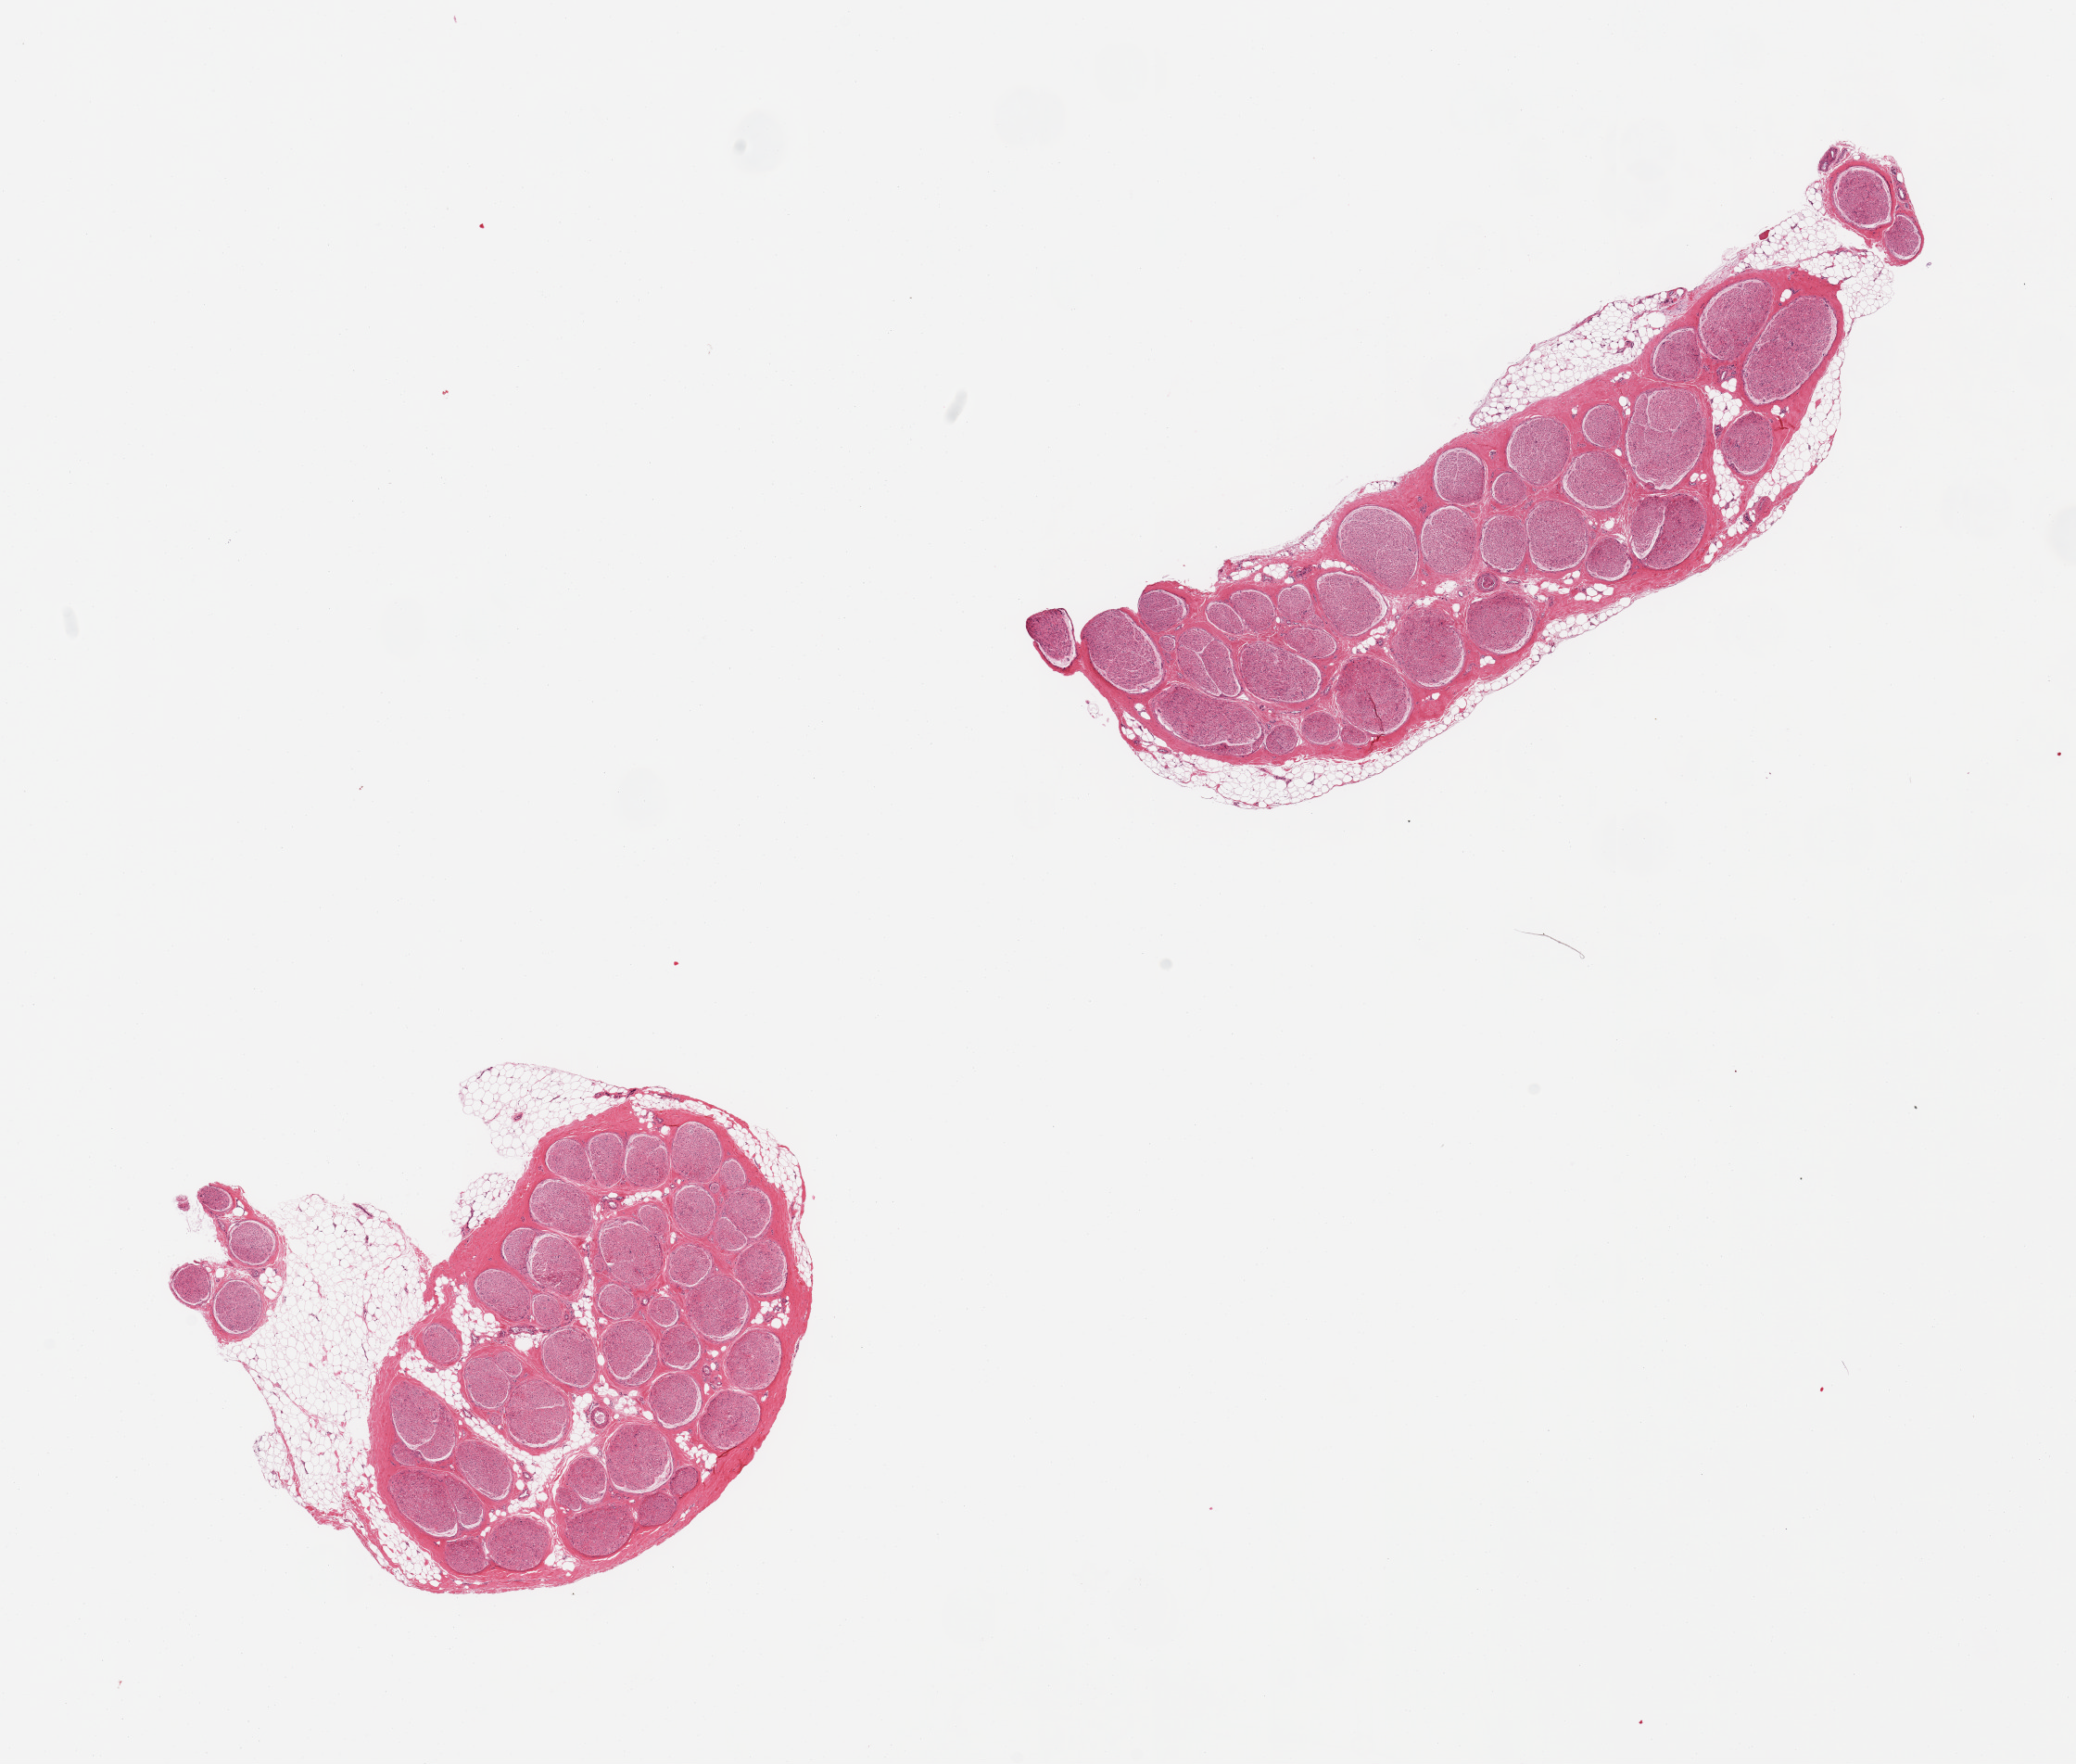
Whole-slide image, haematoxylin and eosin stain, a low-resolution overview of the entire scanned area, about 17.7 x 15.1 mm (acquisition: 20x scan), PAXgene-fixed paraffin-embedded (PFPE) section, target tissue: tibial nerve, tissue donor sample.
- pathologist's review note for this sample: 2 pieces; ~10% surrounding fat